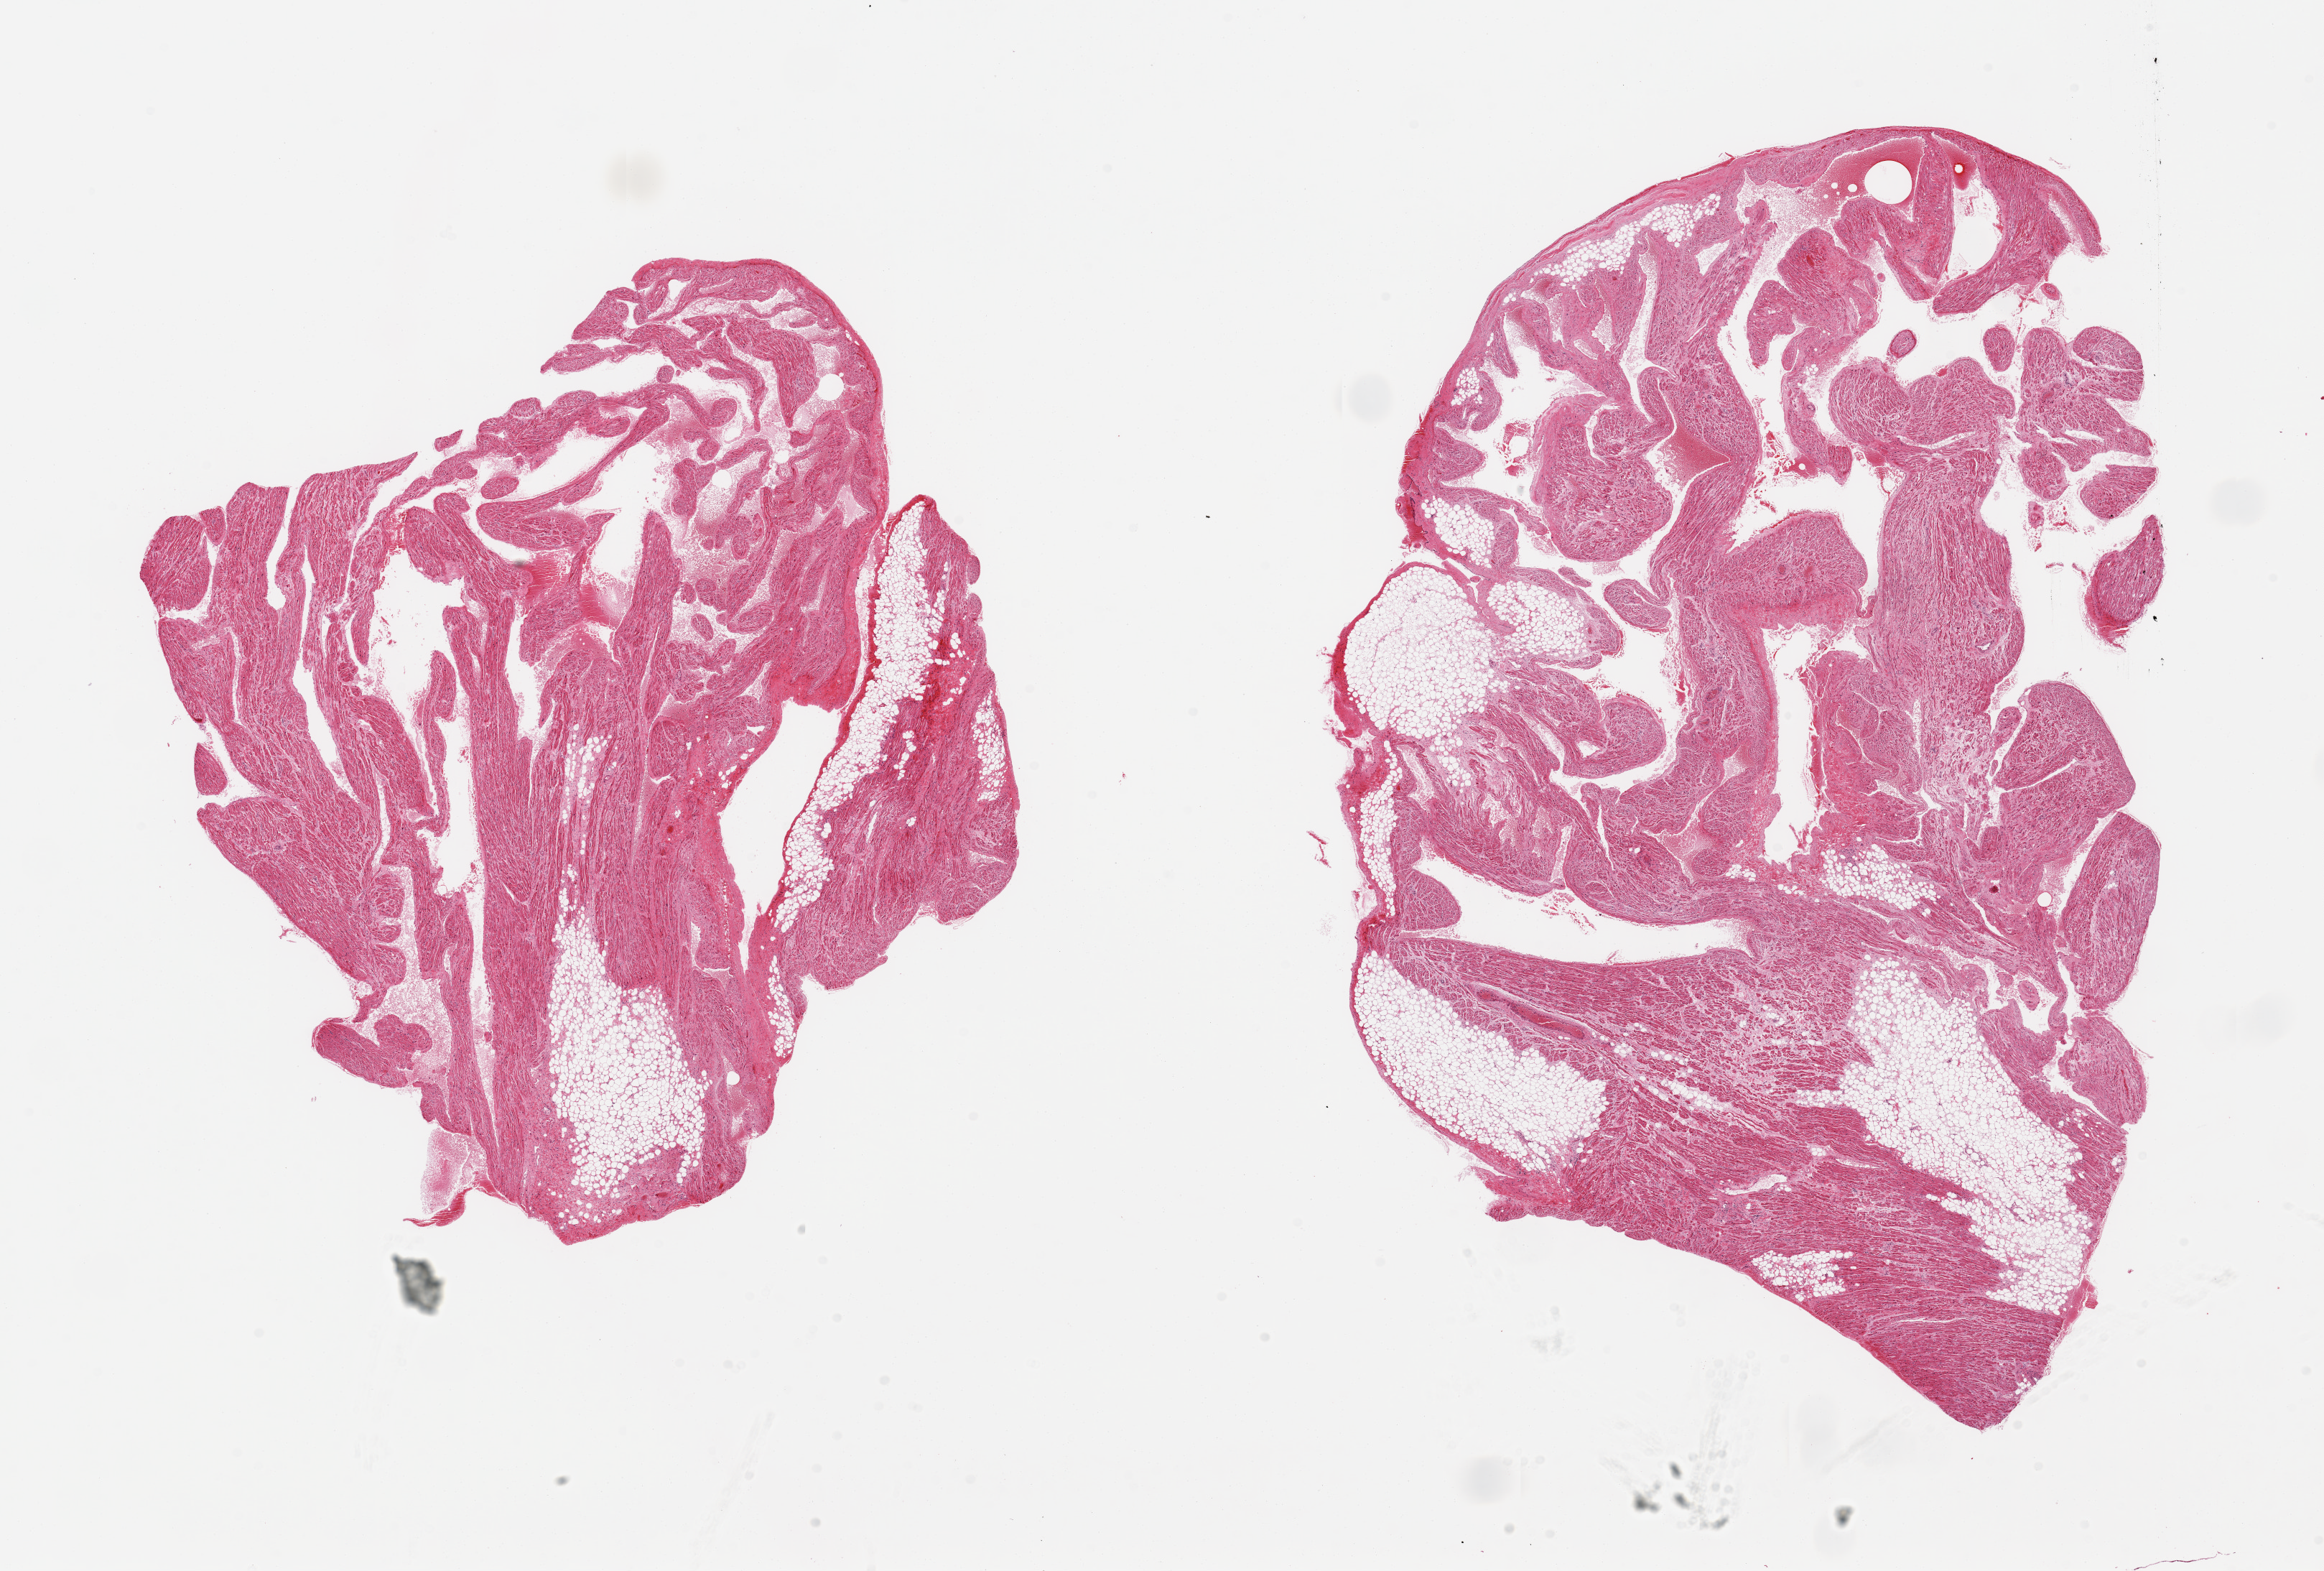
Whole-slide image, haematoxylin and eosin stain, brightfield, whole scanned area (about 25.6 x 17.3 mm) shown as a low-resolution overview, PAXgene-fixed, paraffin-embedded tissue, target tissue: auricular appendage, donor tissue sample. Donor sex: male.
Review note (as recorded): 2 pieces; 30% internal fat content.